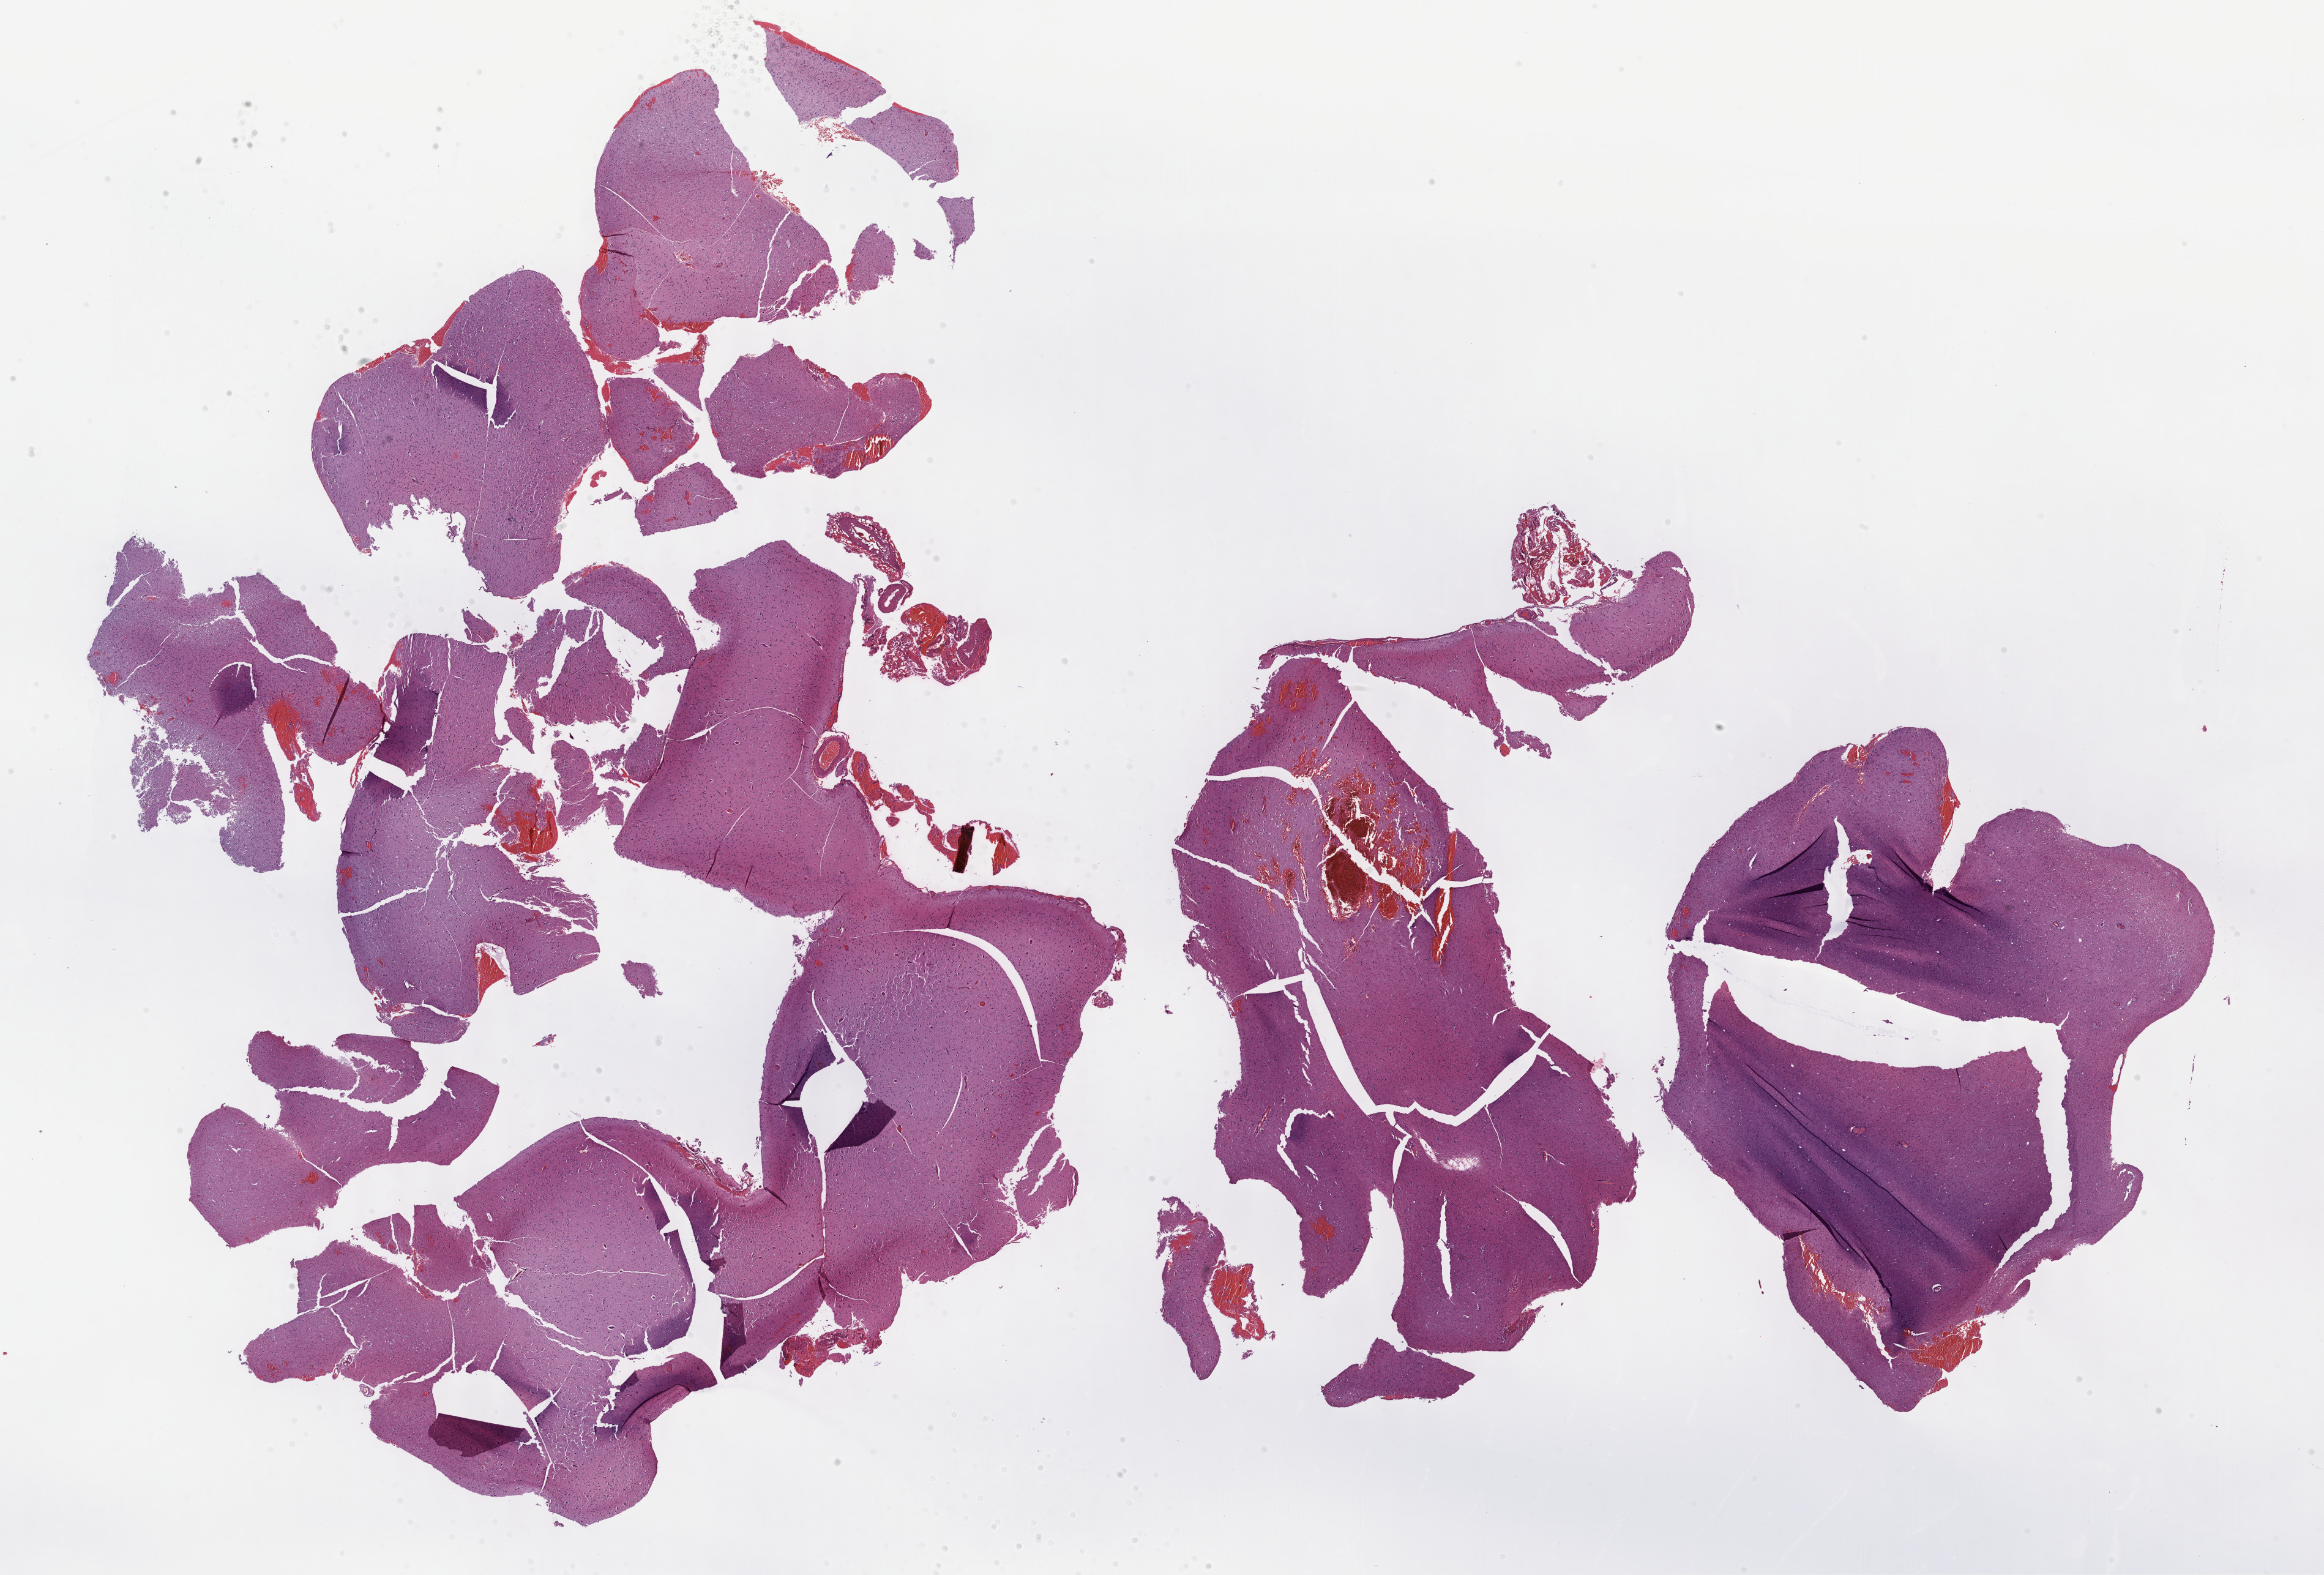
Whole-slide histology image, H&E-stained — whole scanned area (about 30.7 x 20.8 mm, acquisition: 40x scan) shown as a low-resolution overview, FFPE section, primary tumour sample from the brain. Patient: male, age at initial diagnosis 58 years. Histologic grade: G3 (poorly differentiated).
• laterality: right
• histologic diagnosis: Astrocytoma, anaplastic (cerebrum)